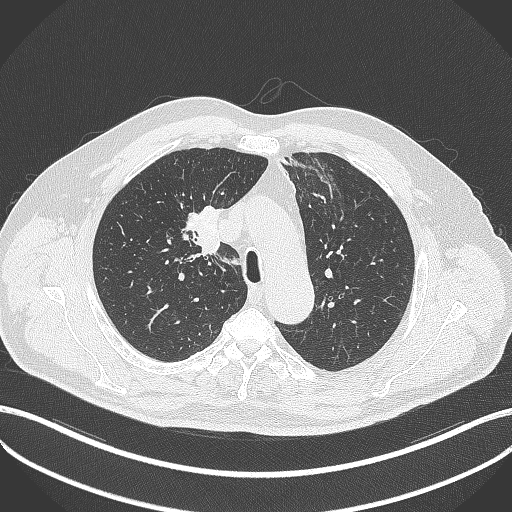
Chest CT, one axial slice. Position 286 of 411 along the scan axis. Reconstruction kernel B70f. Lung window (W 1500 / L -600 HU). 512 × 512 image matrix, field of view 400 × 400 mm. Patient: male, 60 years. Case-level facts recorded for this patient, not image findings: clinical TNM (as recorded): T1b N1 M0.
Annotated regions visible in this slice (rectangle marked by the reading radiologist):
- lung tumour (recorded histology: squamous cell carcinoma): bounding box (x1, y1, x2, y2) in pixels: (183, 196, 223, 268)